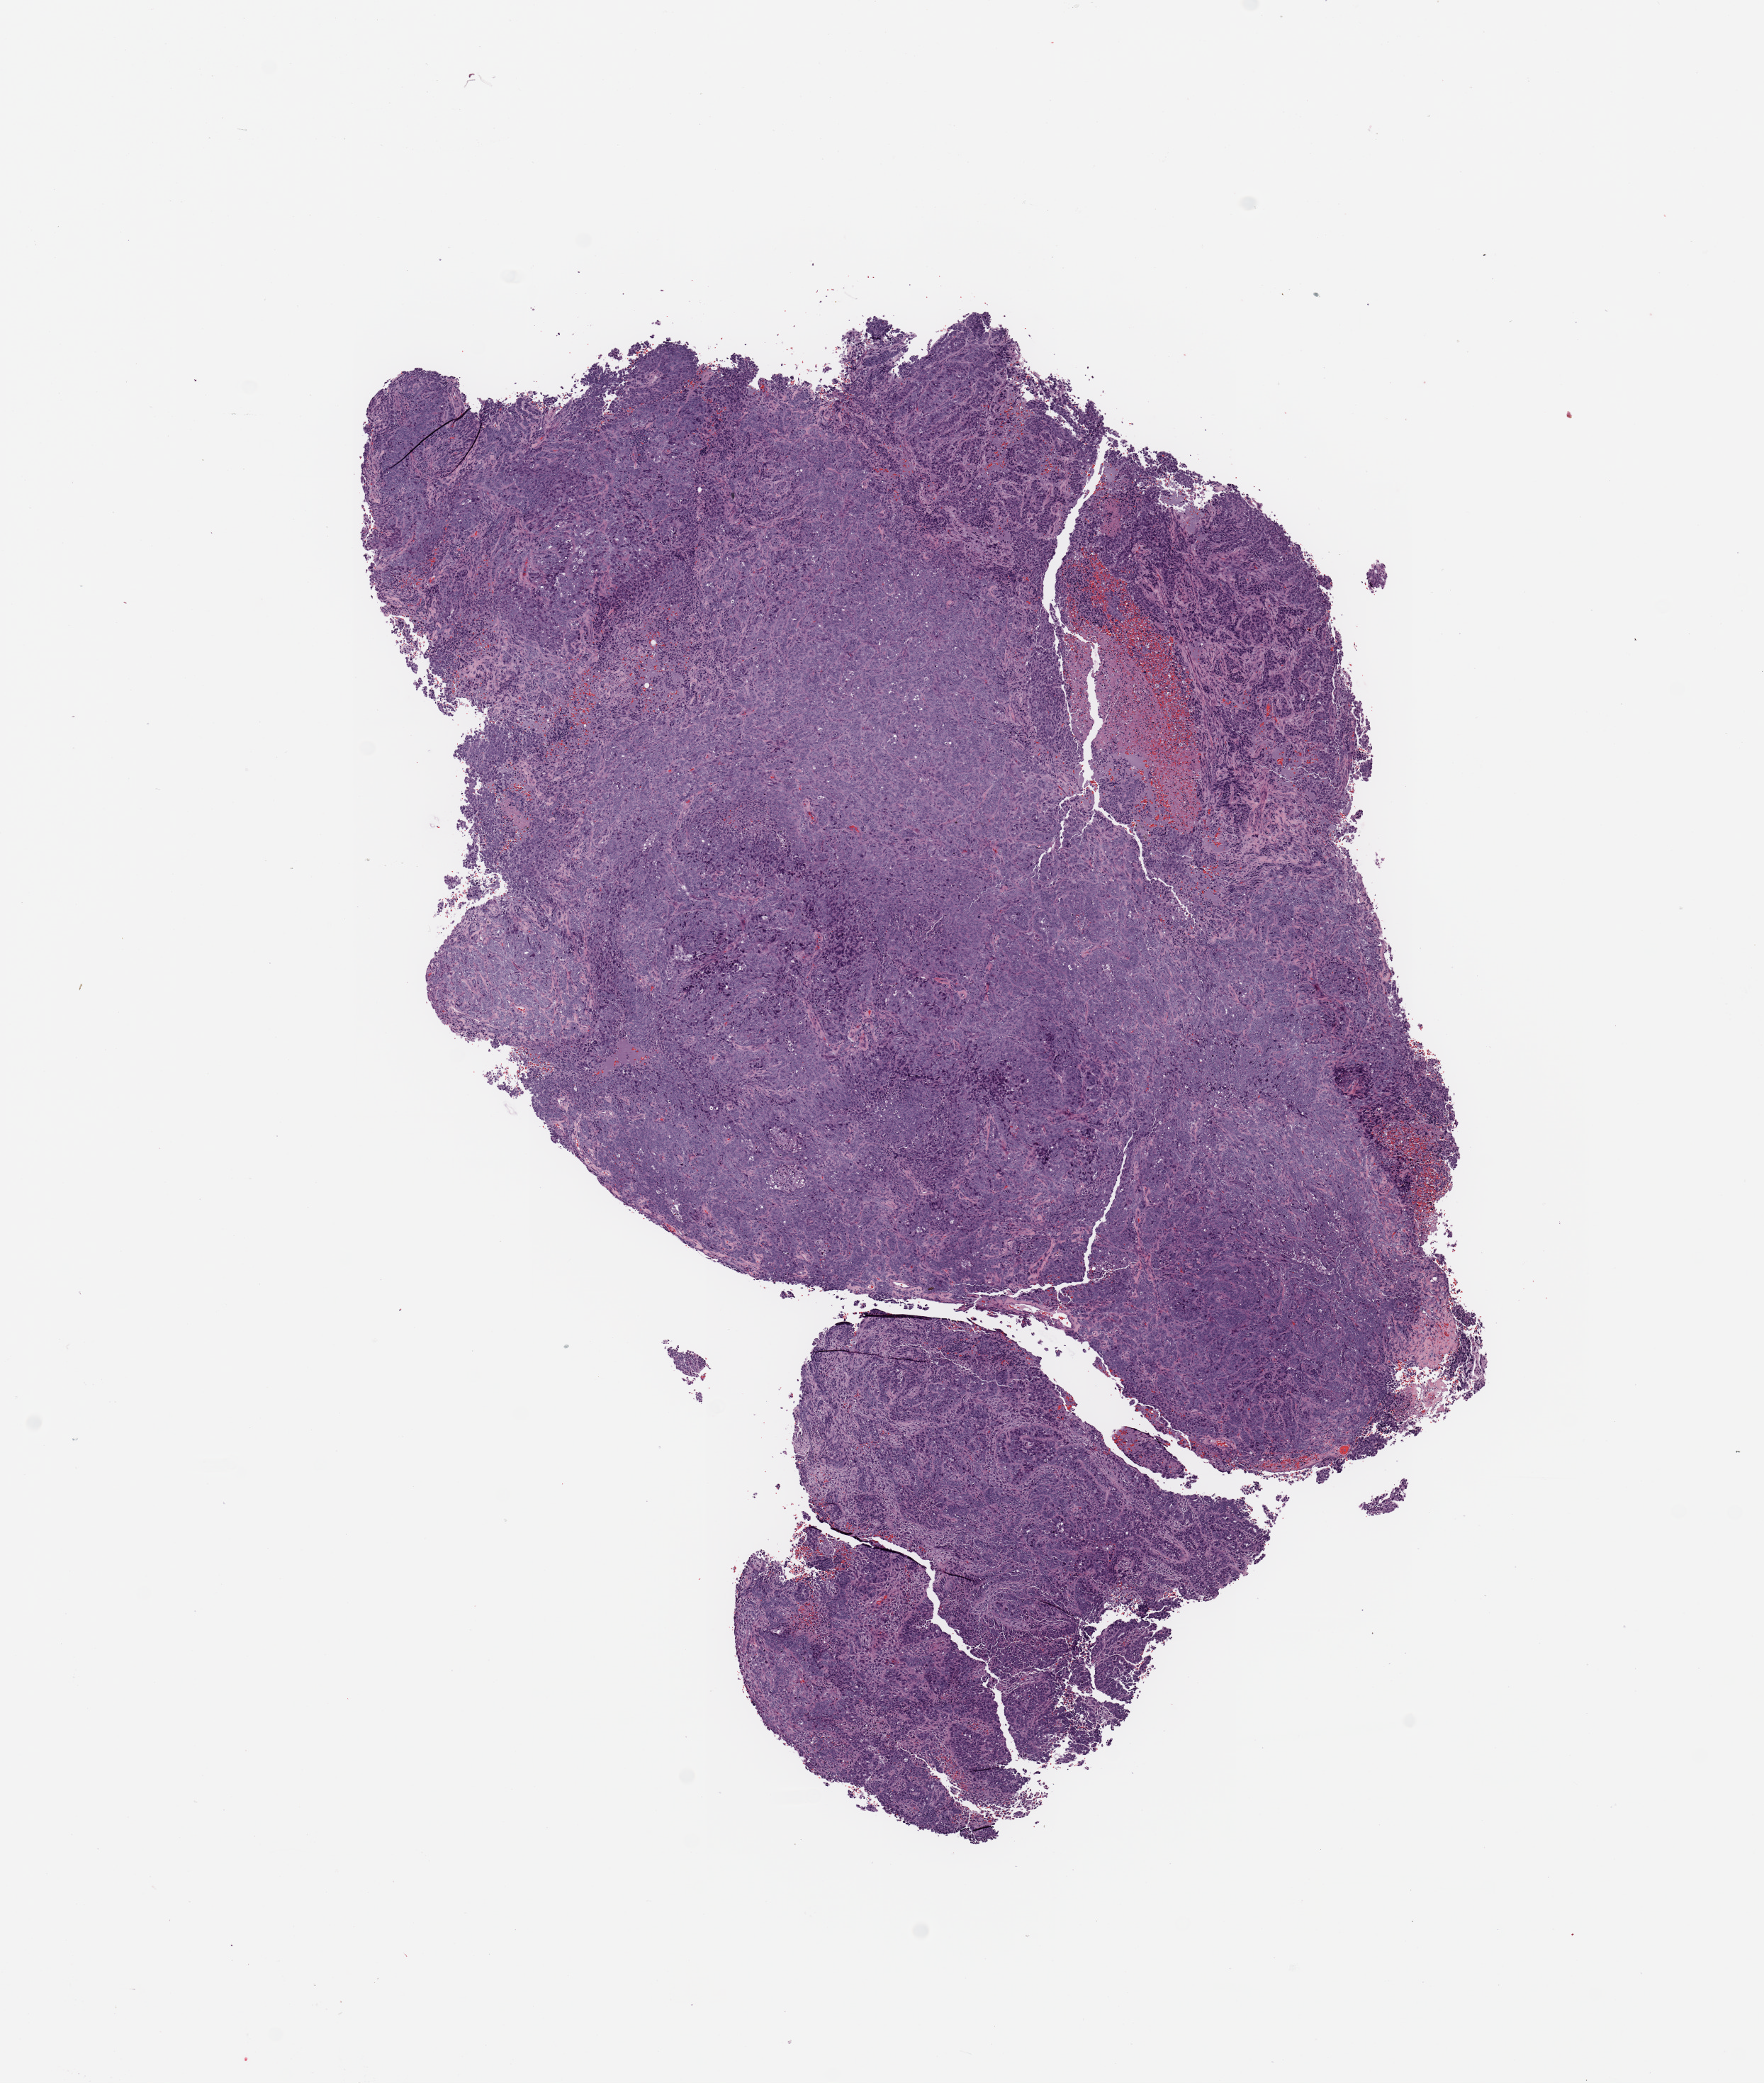
Hematoxylin and eosin (H&E) stained whole-slide image, shown as a low-resolution overview of the whole scanned area (about 9.8 x 11.6 mm, from a 20x scan); uterus, tumour tissue. Patient: female, age 68 years. Histologic grade: G3 (poorly differentiated).
* AJCC pathologic stage: III
* diagnosis: Endometrioid adenocarcinoma, NOS